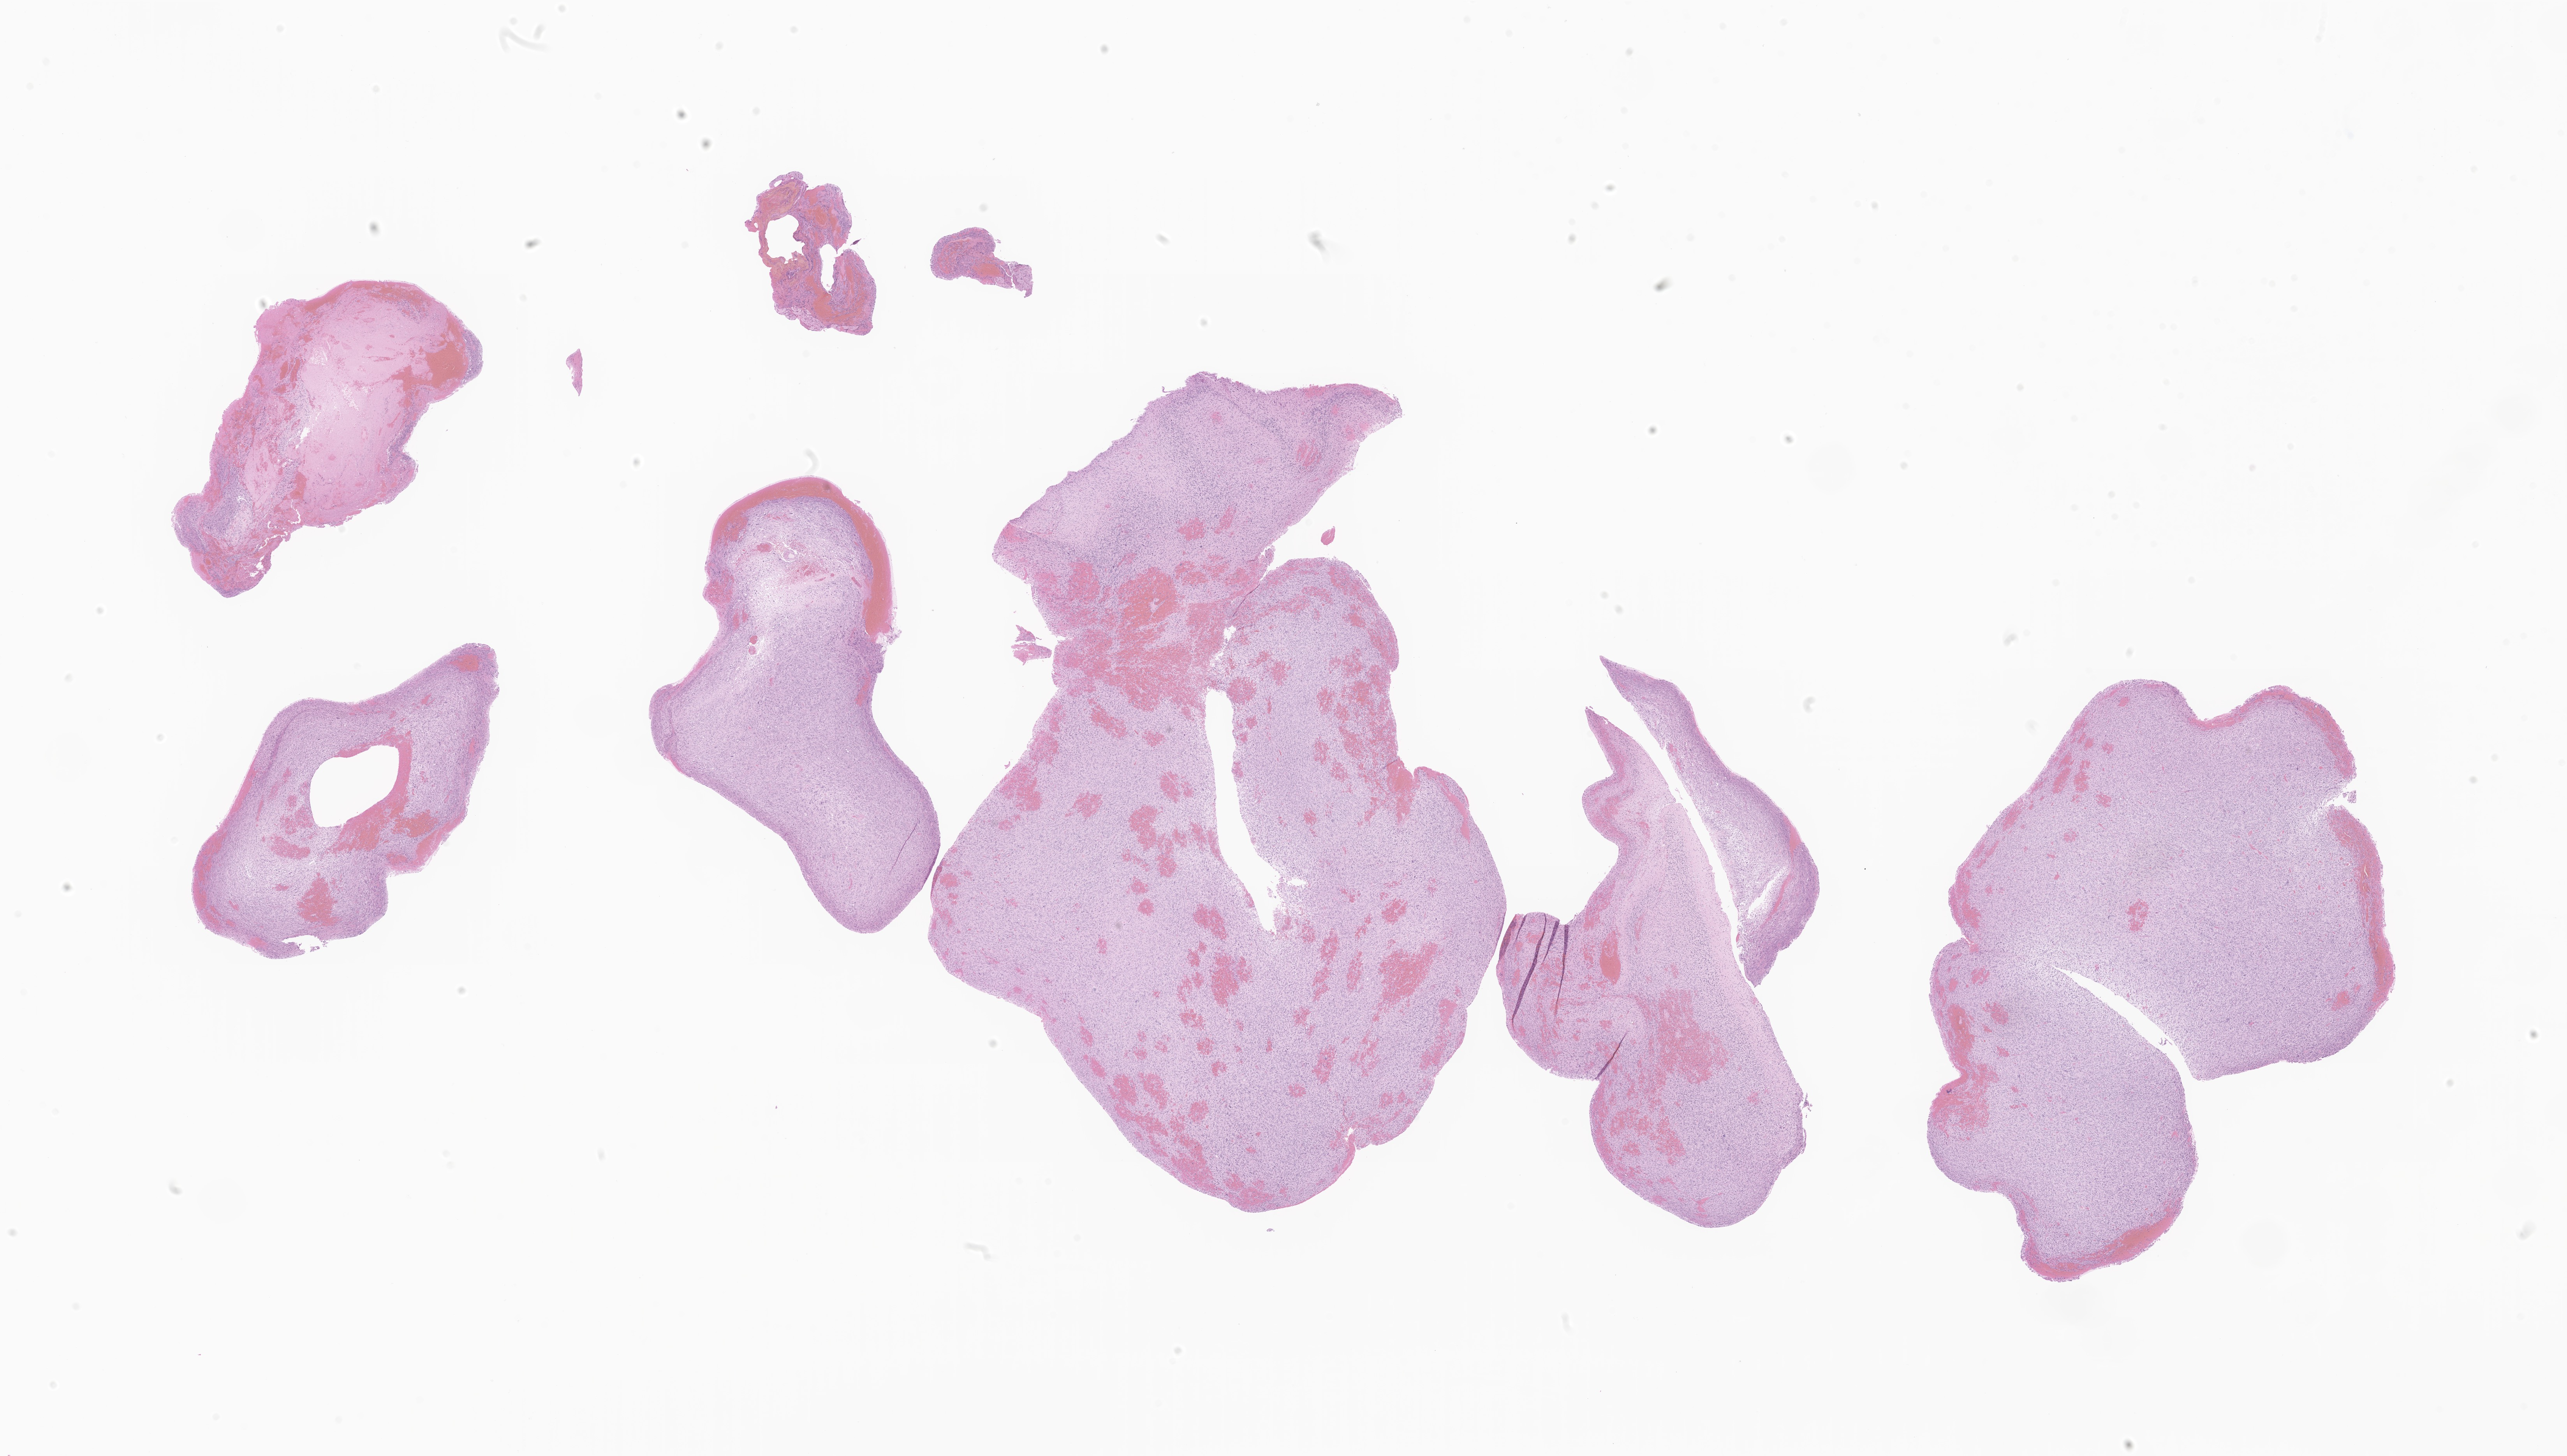
Whole-slide image, H&E stain of tumor tissue from the brain, a low-resolution overview of the entire scanned area, about 27.8 x 15.8 mm, formalin-fixed, paraffin-embedded (FFPE) tissue. Patient male; age 64 months (5 years 4 months).
* diagnosis (ICD-O-3 morphology term): Glioma, malignant